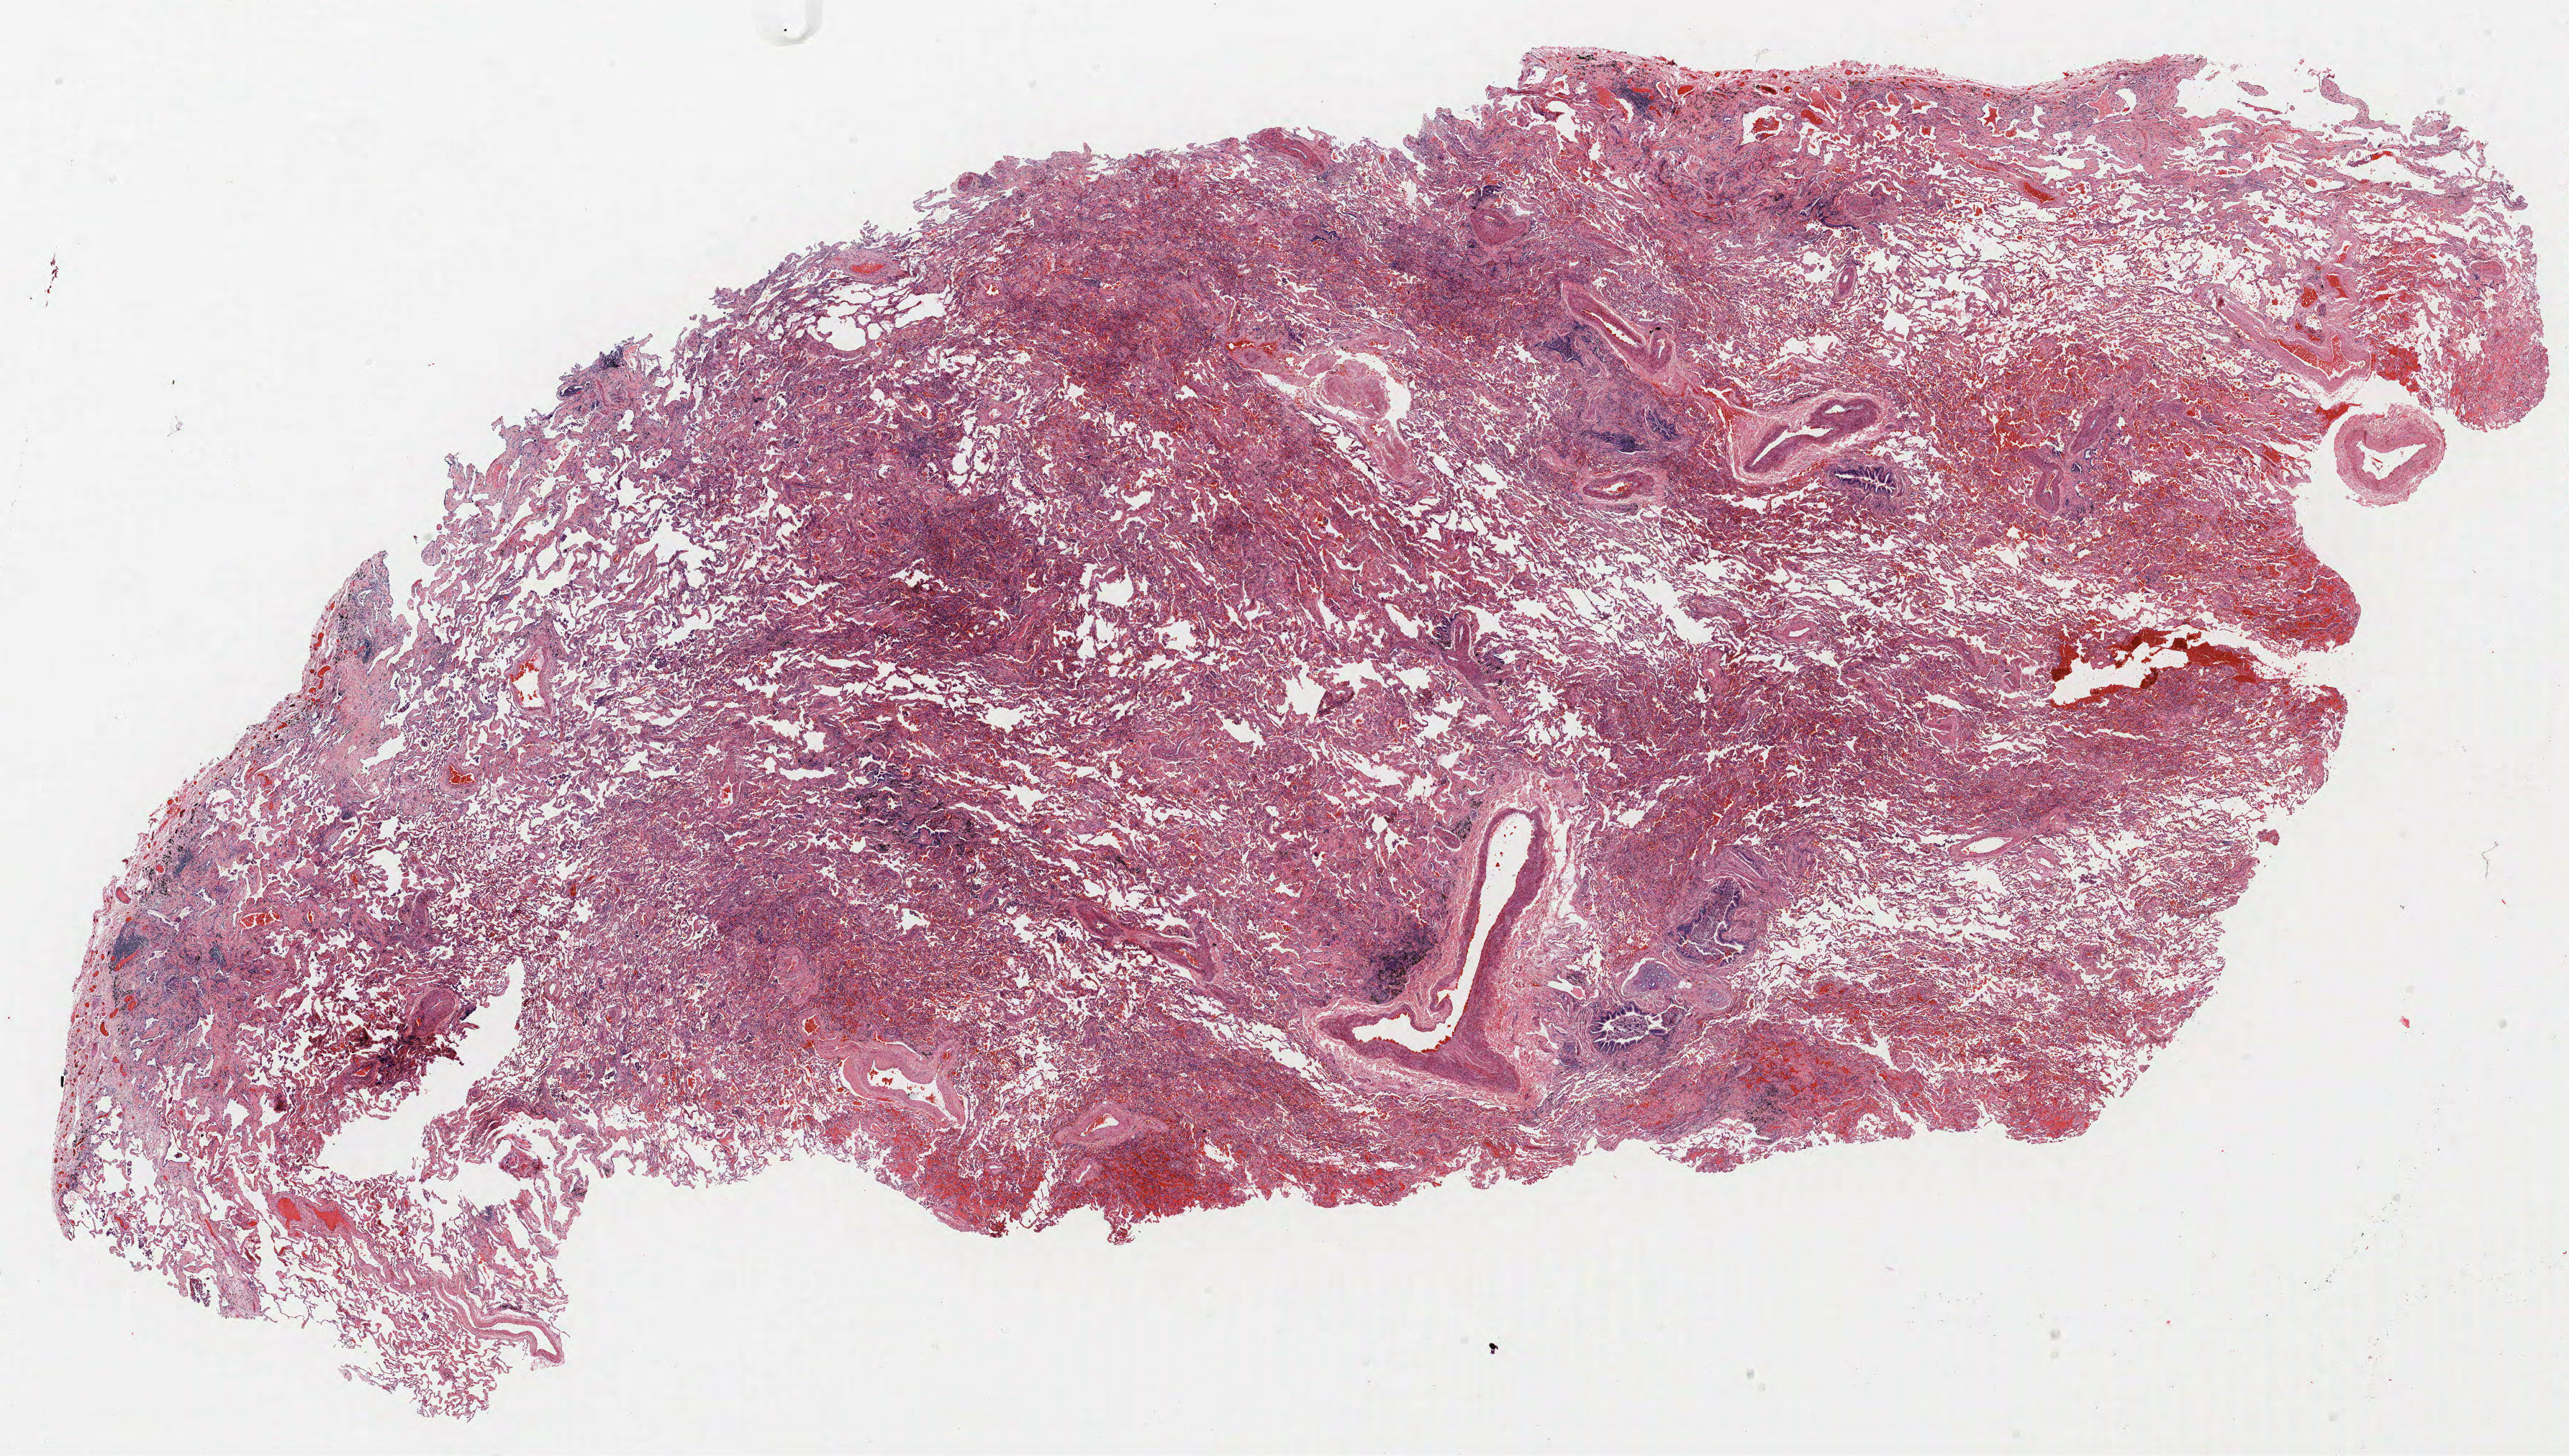
Whole-slide histology image, H&E-stained, low-resolution overview of the scanned area, about 28.6 x 16.2 mm (from a 40x scan), formalin-fixed paraffin-embedded (FFPE) section, lung. Male patient, aged 59 at enrolment. Current smoker at enrolment.
Participant's lung-cancer diagnosis: Adenocarcinoma, NOS (ICD-O-3 8140/3). Note: participant had 2 primary lung cancers recorded; fields above describe the first.